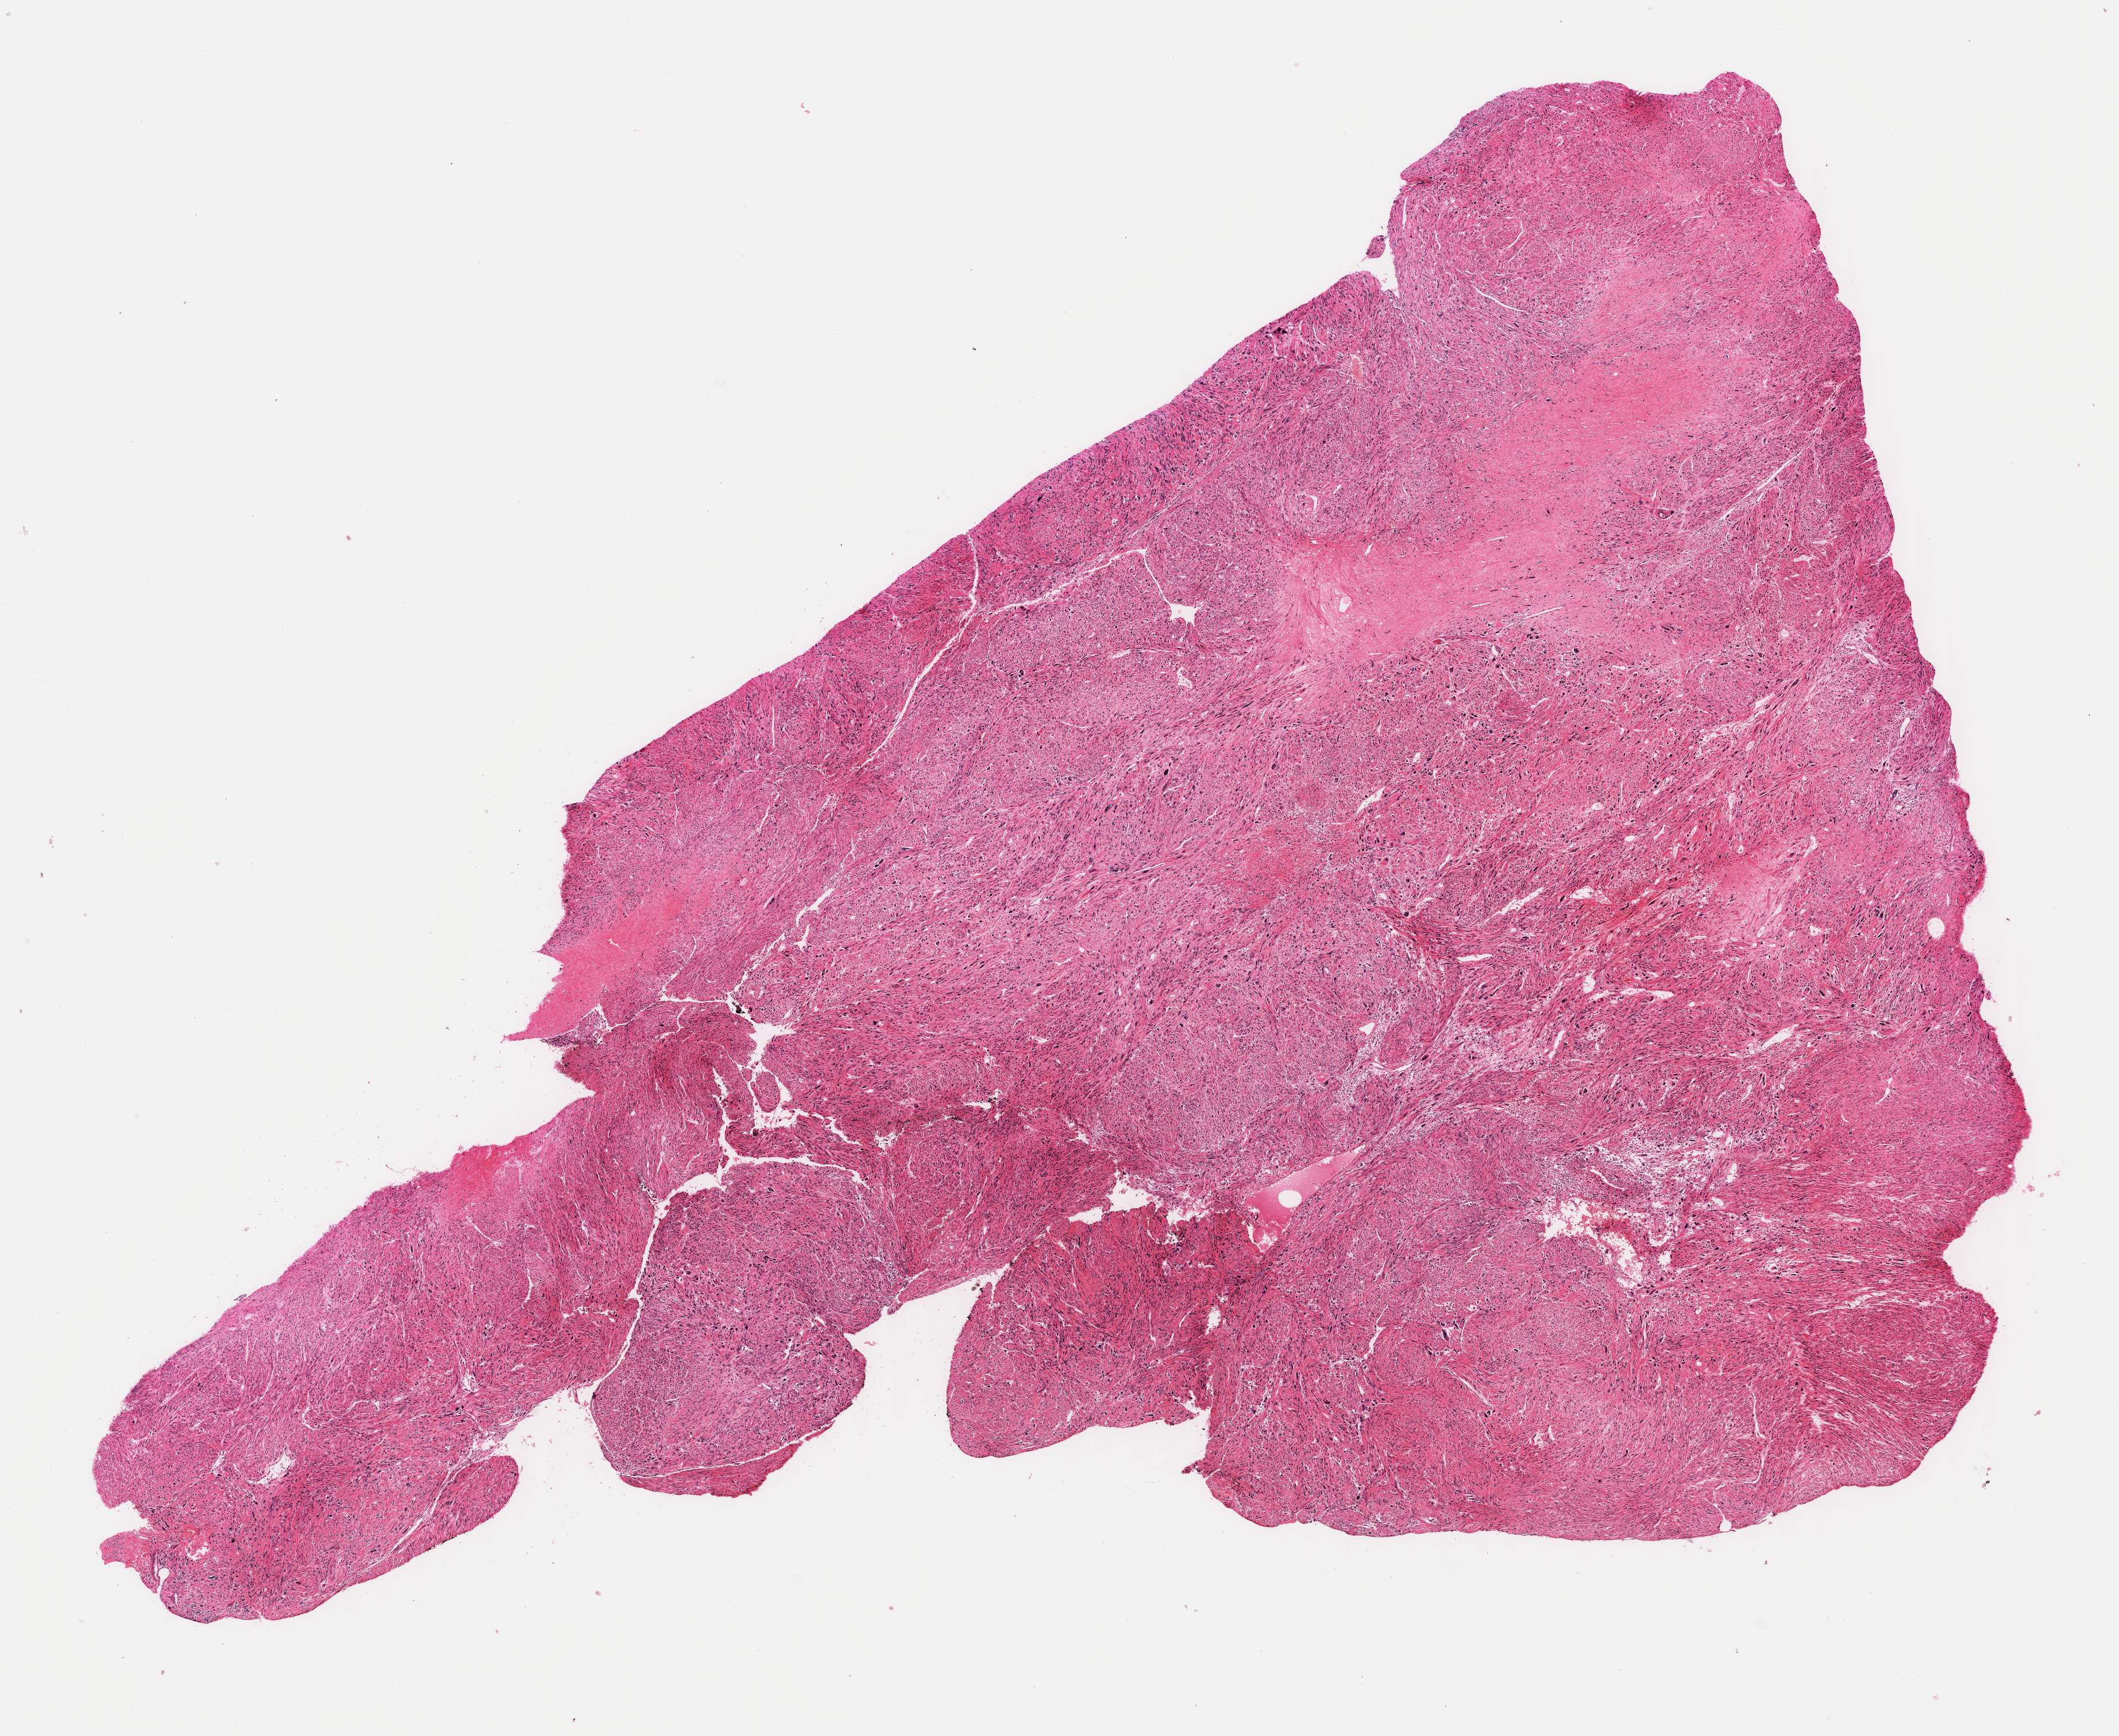
H&E-stained whole-slide image — a low-resolution overview of the entire scanned area, about 14.5 x 11.9 mm (slide scanned at 40x). Formalin-fixed paraffin-embedded (FFPE) diagnostic section. Retroperitoneum and peritoneum, primary tumour sample. Female, age 72 years at initial diagnosis.
* pathologic diagnosis: Leiomyosarcoma, NOS